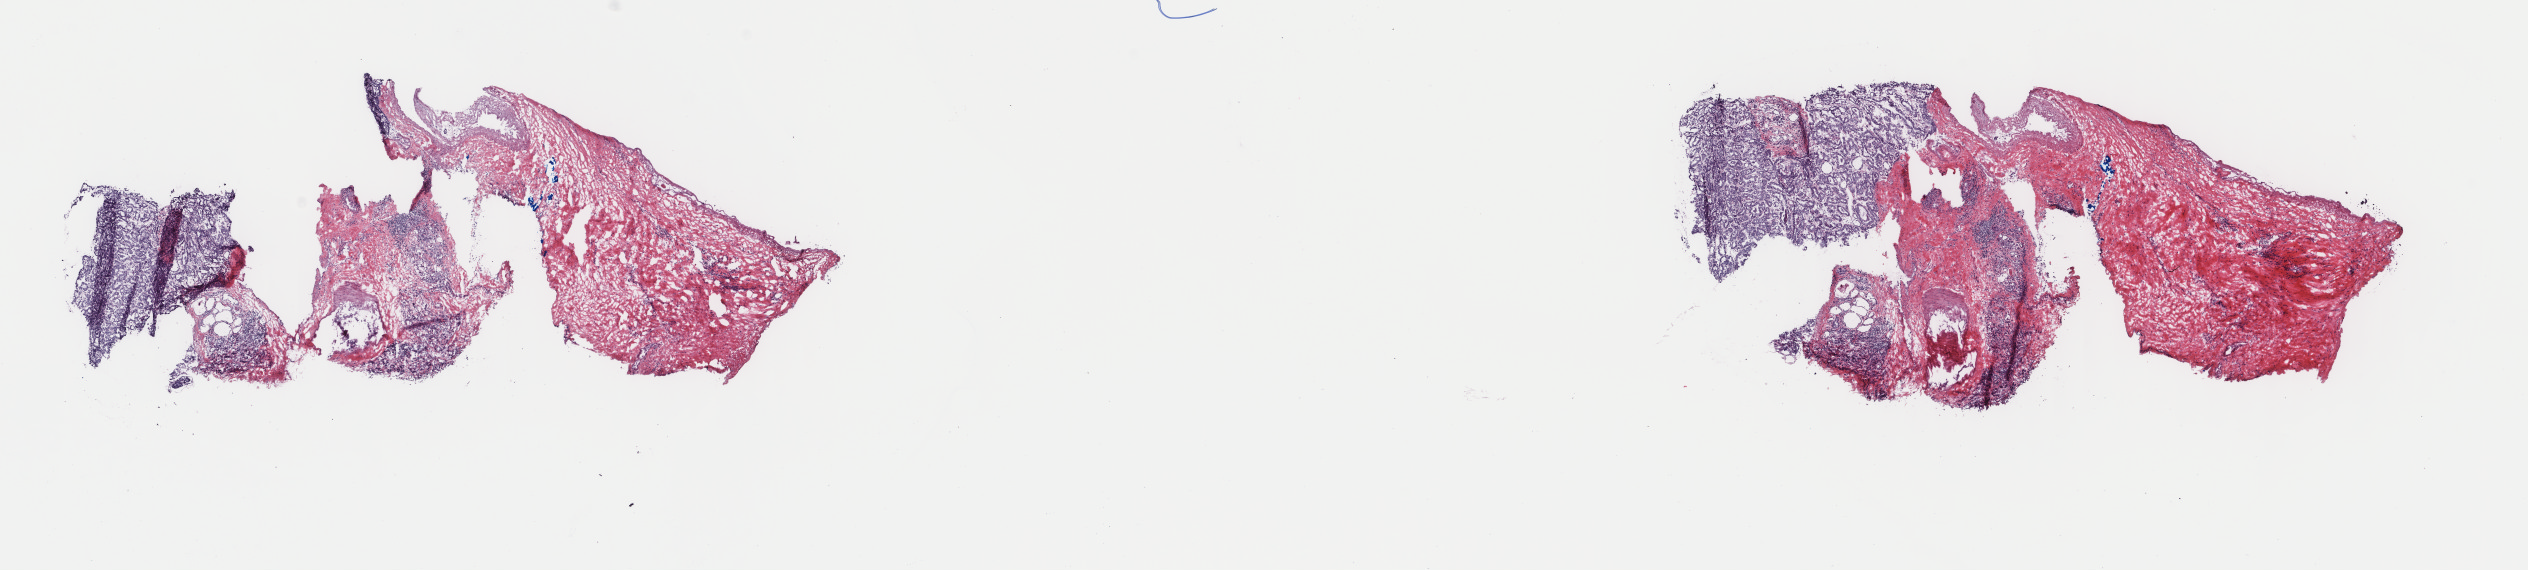
Whole-slide histology image, Hematoxylin and eosin (H&E) stained, whole scanned area (about 20.1 x 4.5 mm, acquisition: 40x scan) shown as a low-resolution overview, frozen section, primary tumour sample from the thyroid. Patient: female, age at initial diagnosis 61 years. Pathologist review of this section (percent, as recorded): tumour cells 40%, tumour nuclei 90%, normal cells 10%, stromal cells 50%, necrosis 0%. Infiltration values recorded for this section: lymphocyte infiltration 6%, monocyte infiltration 1%, neutrophil infiltration 0%.
Laterality: bilateral. AJCC pathologic stage: III (7th edition). Lymph nodes positive (case pathology): 1 of 4 examined. Pathologic diagnosis: Papillary adenocarcinoma, NOS (thyroid gland). TNM: T2 N1 M0.